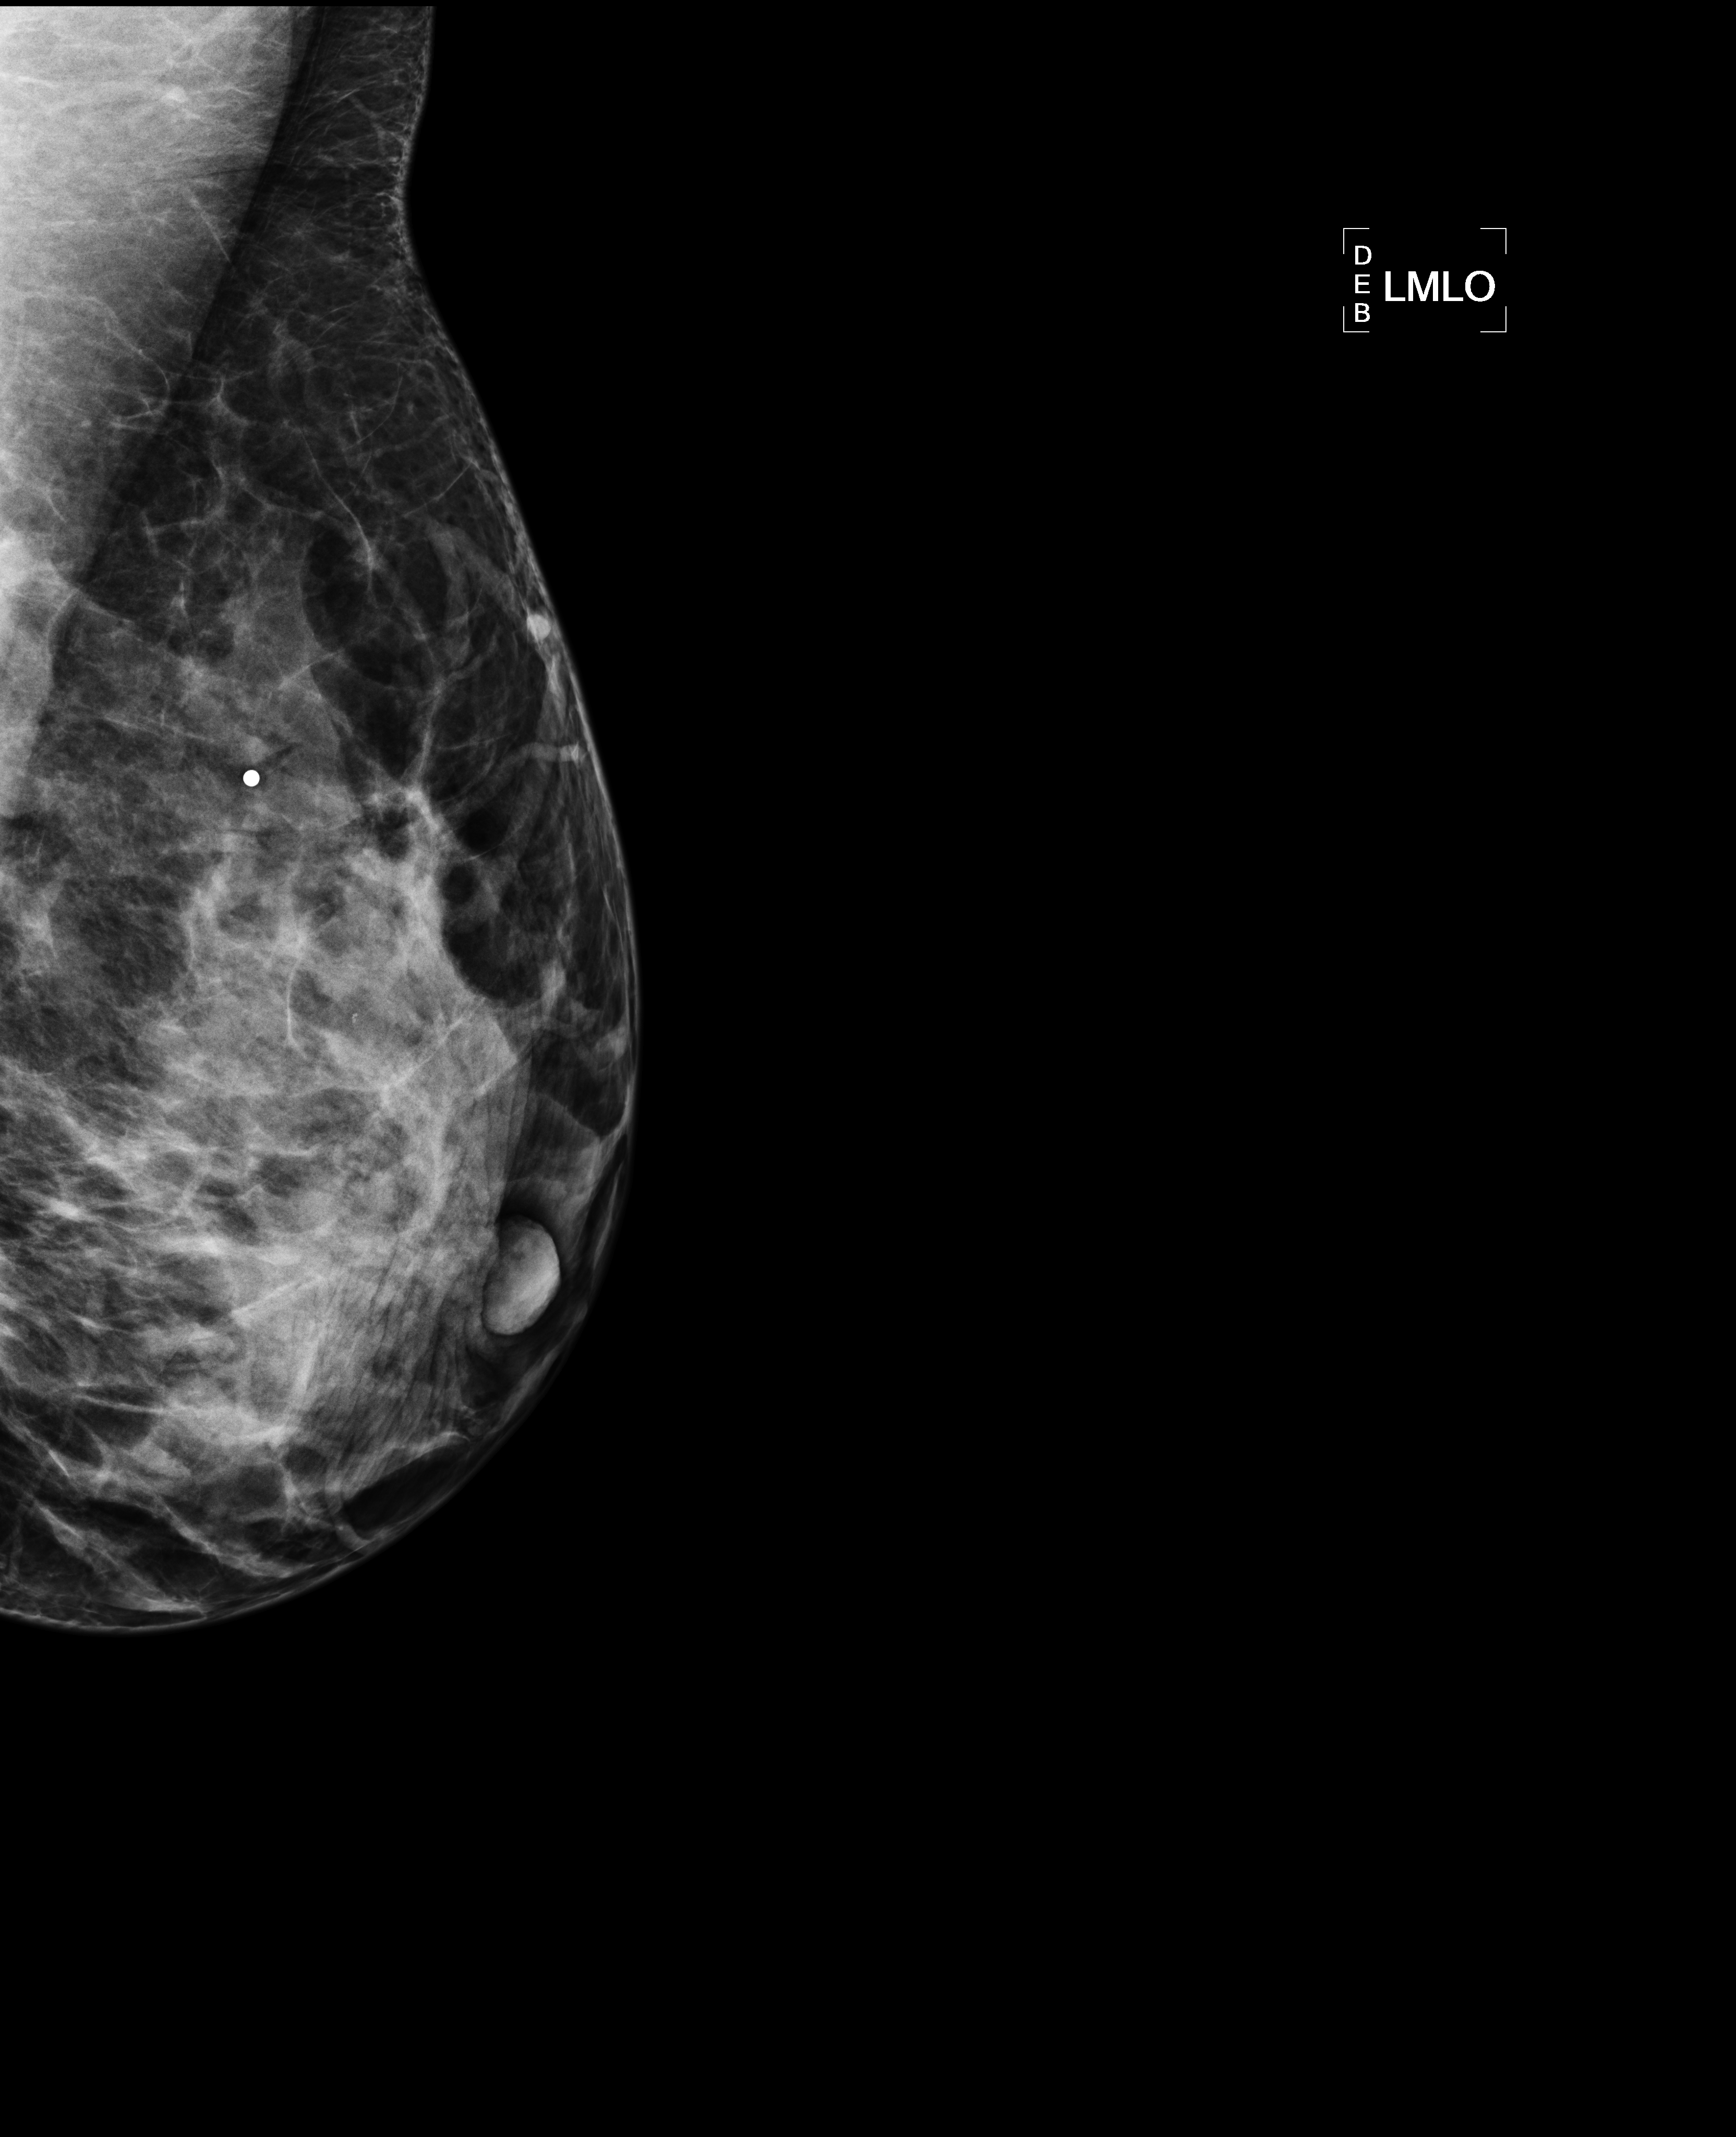
Mammogram, left breast, MLO view.
Patient-level pathology facts (clinical record, not image findings): pathology diagnosis: INVASIVE DUCTAL CARCINOMA, MODIFIED SCARFF-BLOOM-RICHARDSON GRADE-I/III. A LESS THAN 5% INTRADUCTAL CARCINOMA COMPONENT, NUCLEAR GRADE-II/III, IS ALSO PRESENT. (left breast); receptor status (as recorded): ER pos (strong), PR pos (strong), HER2 pos; pathology report notes: mastectomy; INVASIVE DUCTAL CARCINOMA, MODIFIED SCARFF-BLOOM-RICHARDSON GRADE-I/III. A LESS THAN 5% INTRADUCTAL CARCINOMA COMPONENT, NUCLEAR GRADE-II/III, IS ALSO PRESENT; clinical background (as recorded): early 40s with left breast cancer. LMP unknown.